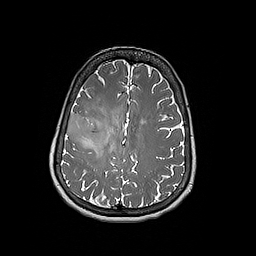
Brain MRI from a brain-tumour surgery series, one axial slice. Slice 71 of 192 in the series (ordered by position). 1 mm slice thickness. 256 × 256 image matrix, field of view 250 × 250 mm. From the clinical record (not read from this slice): histopathology: Oligodendroglioma; WHO grade: 3; IDH mutation: yes; tumour location: Right Frontal.
Structures marked on this image (outlined manually by an expert reader):
- tumour: box from (x=67, y=113) to (x=110, y=149) px